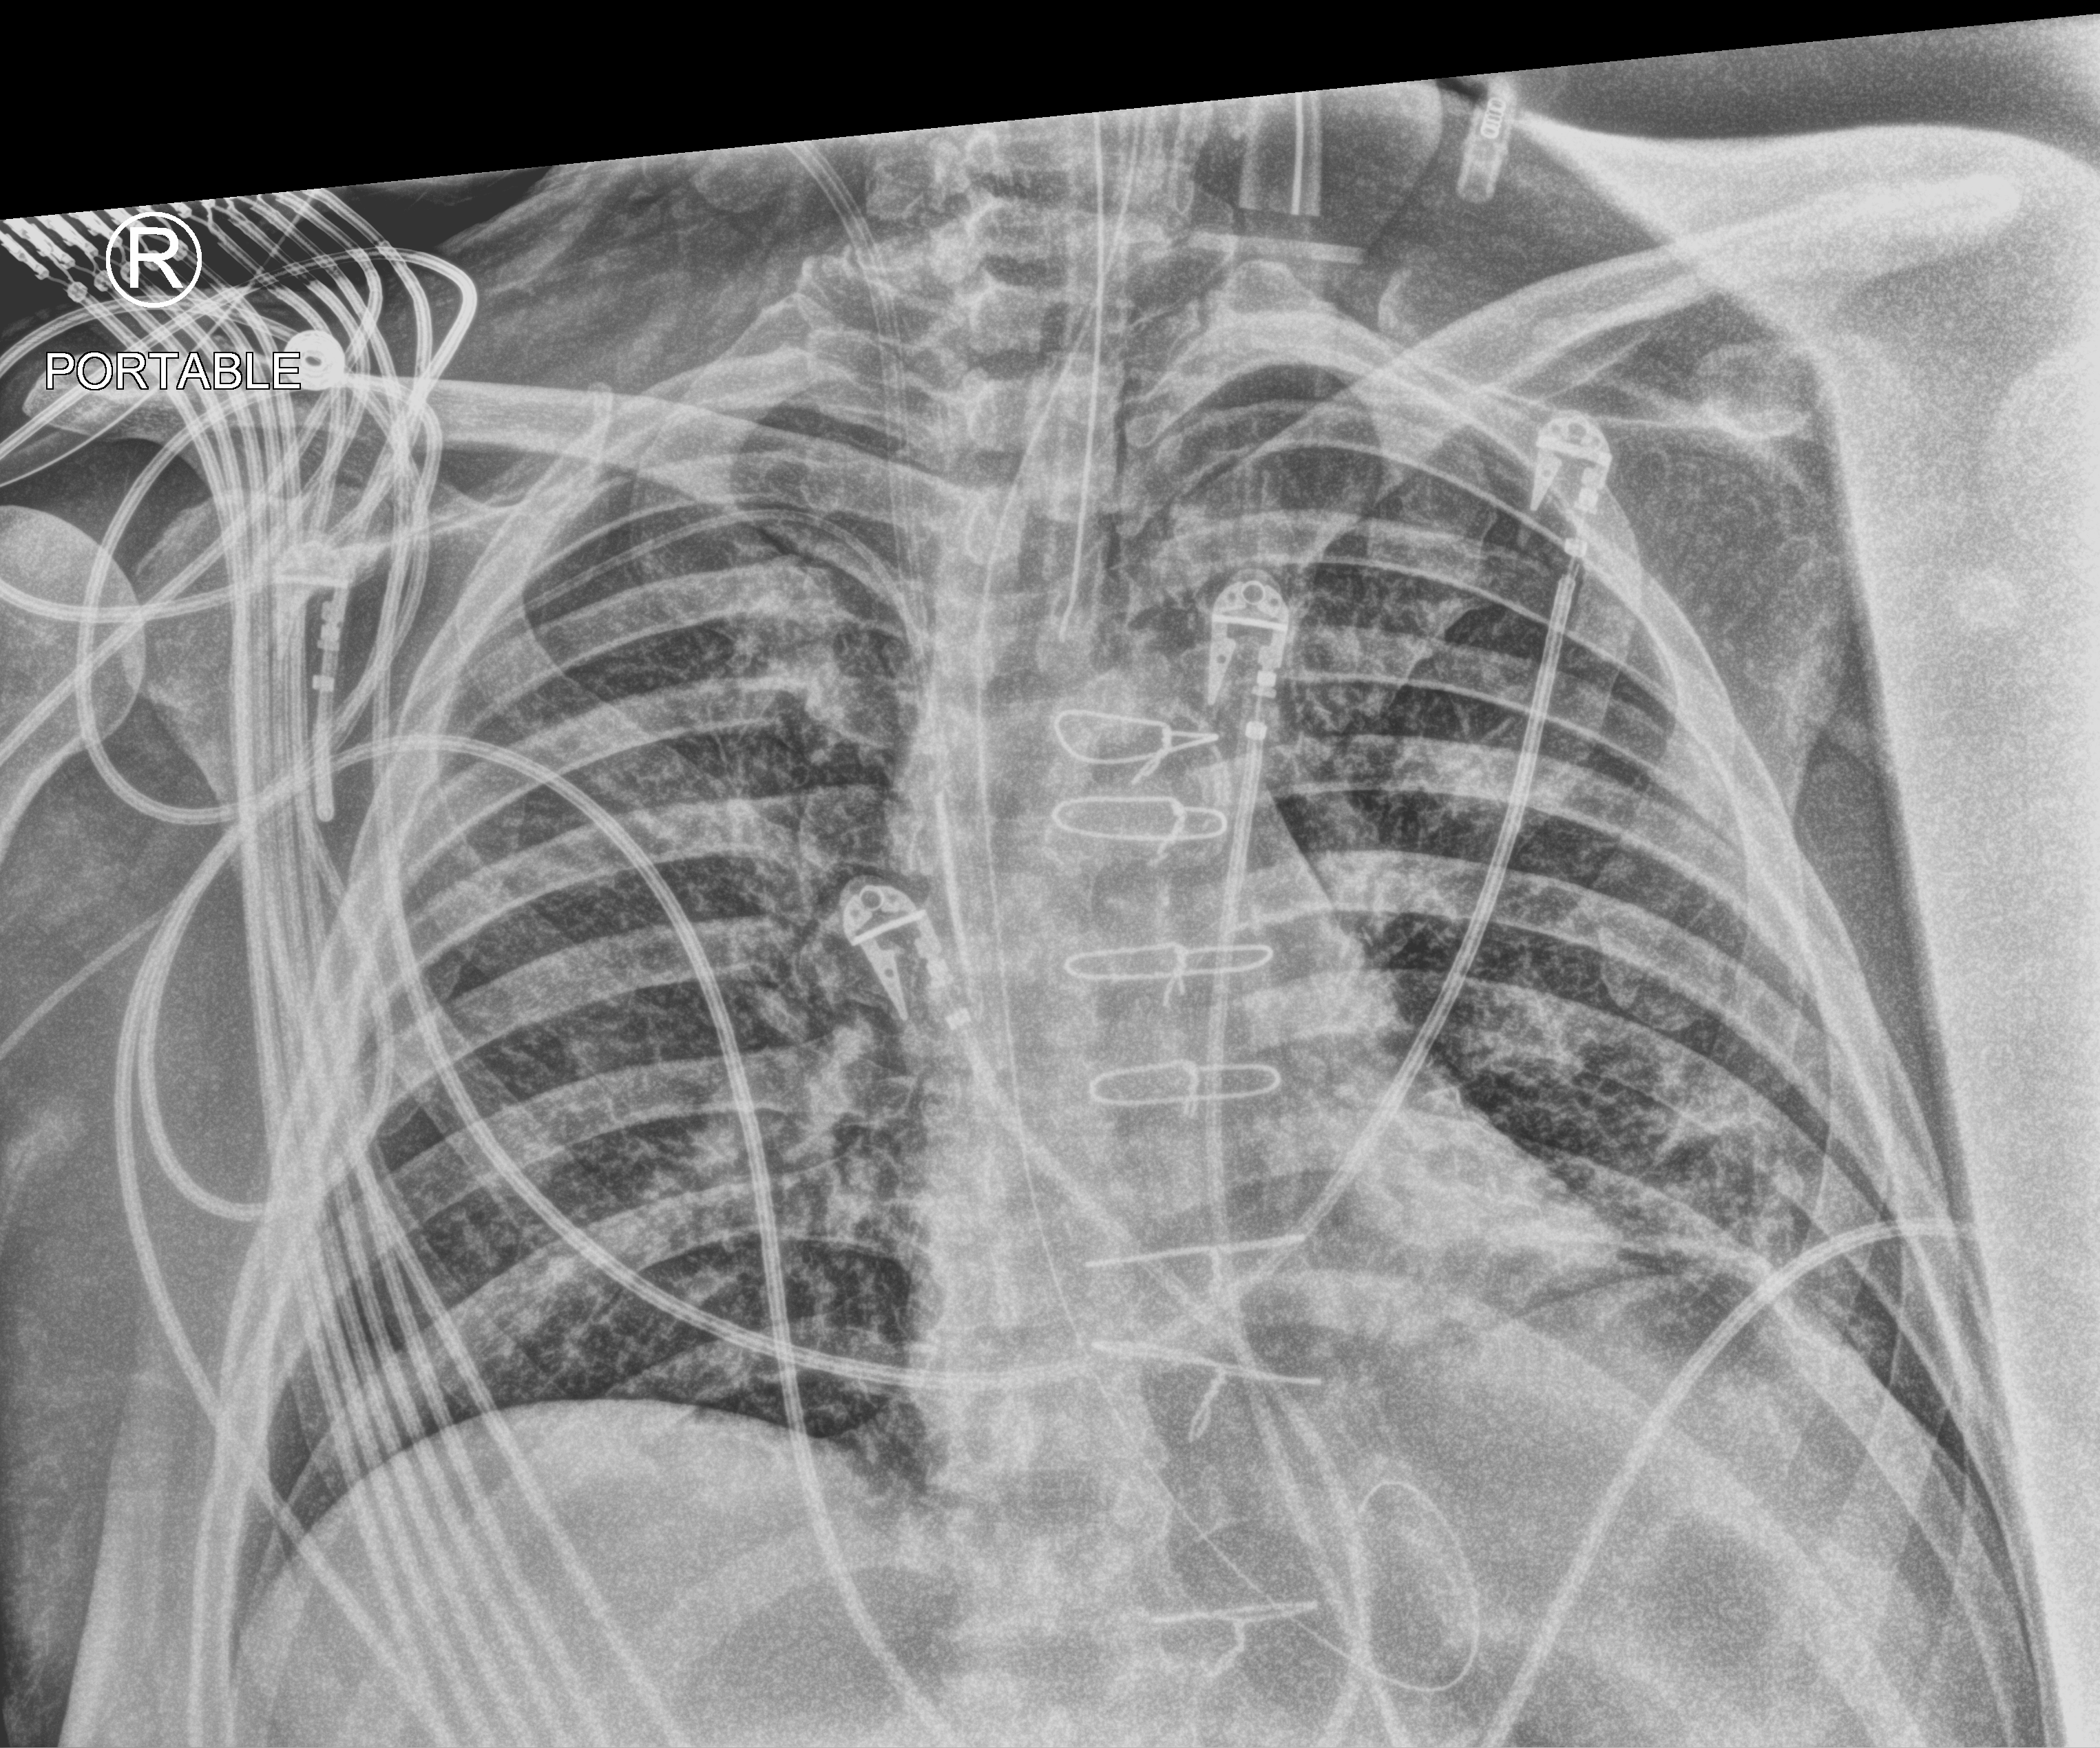
Chest X-ray (portable); anteroposterior (AP) projection. Patient hospitalised with COVID-19; male, aged 60–74 years.
Admission-level facts for this patient (not findings on this image; timing relative to this image not recorded): hypertension (admission record): yes; mechanically ventilated during this hospital stay: yes; length of hospital stay: 44 days.